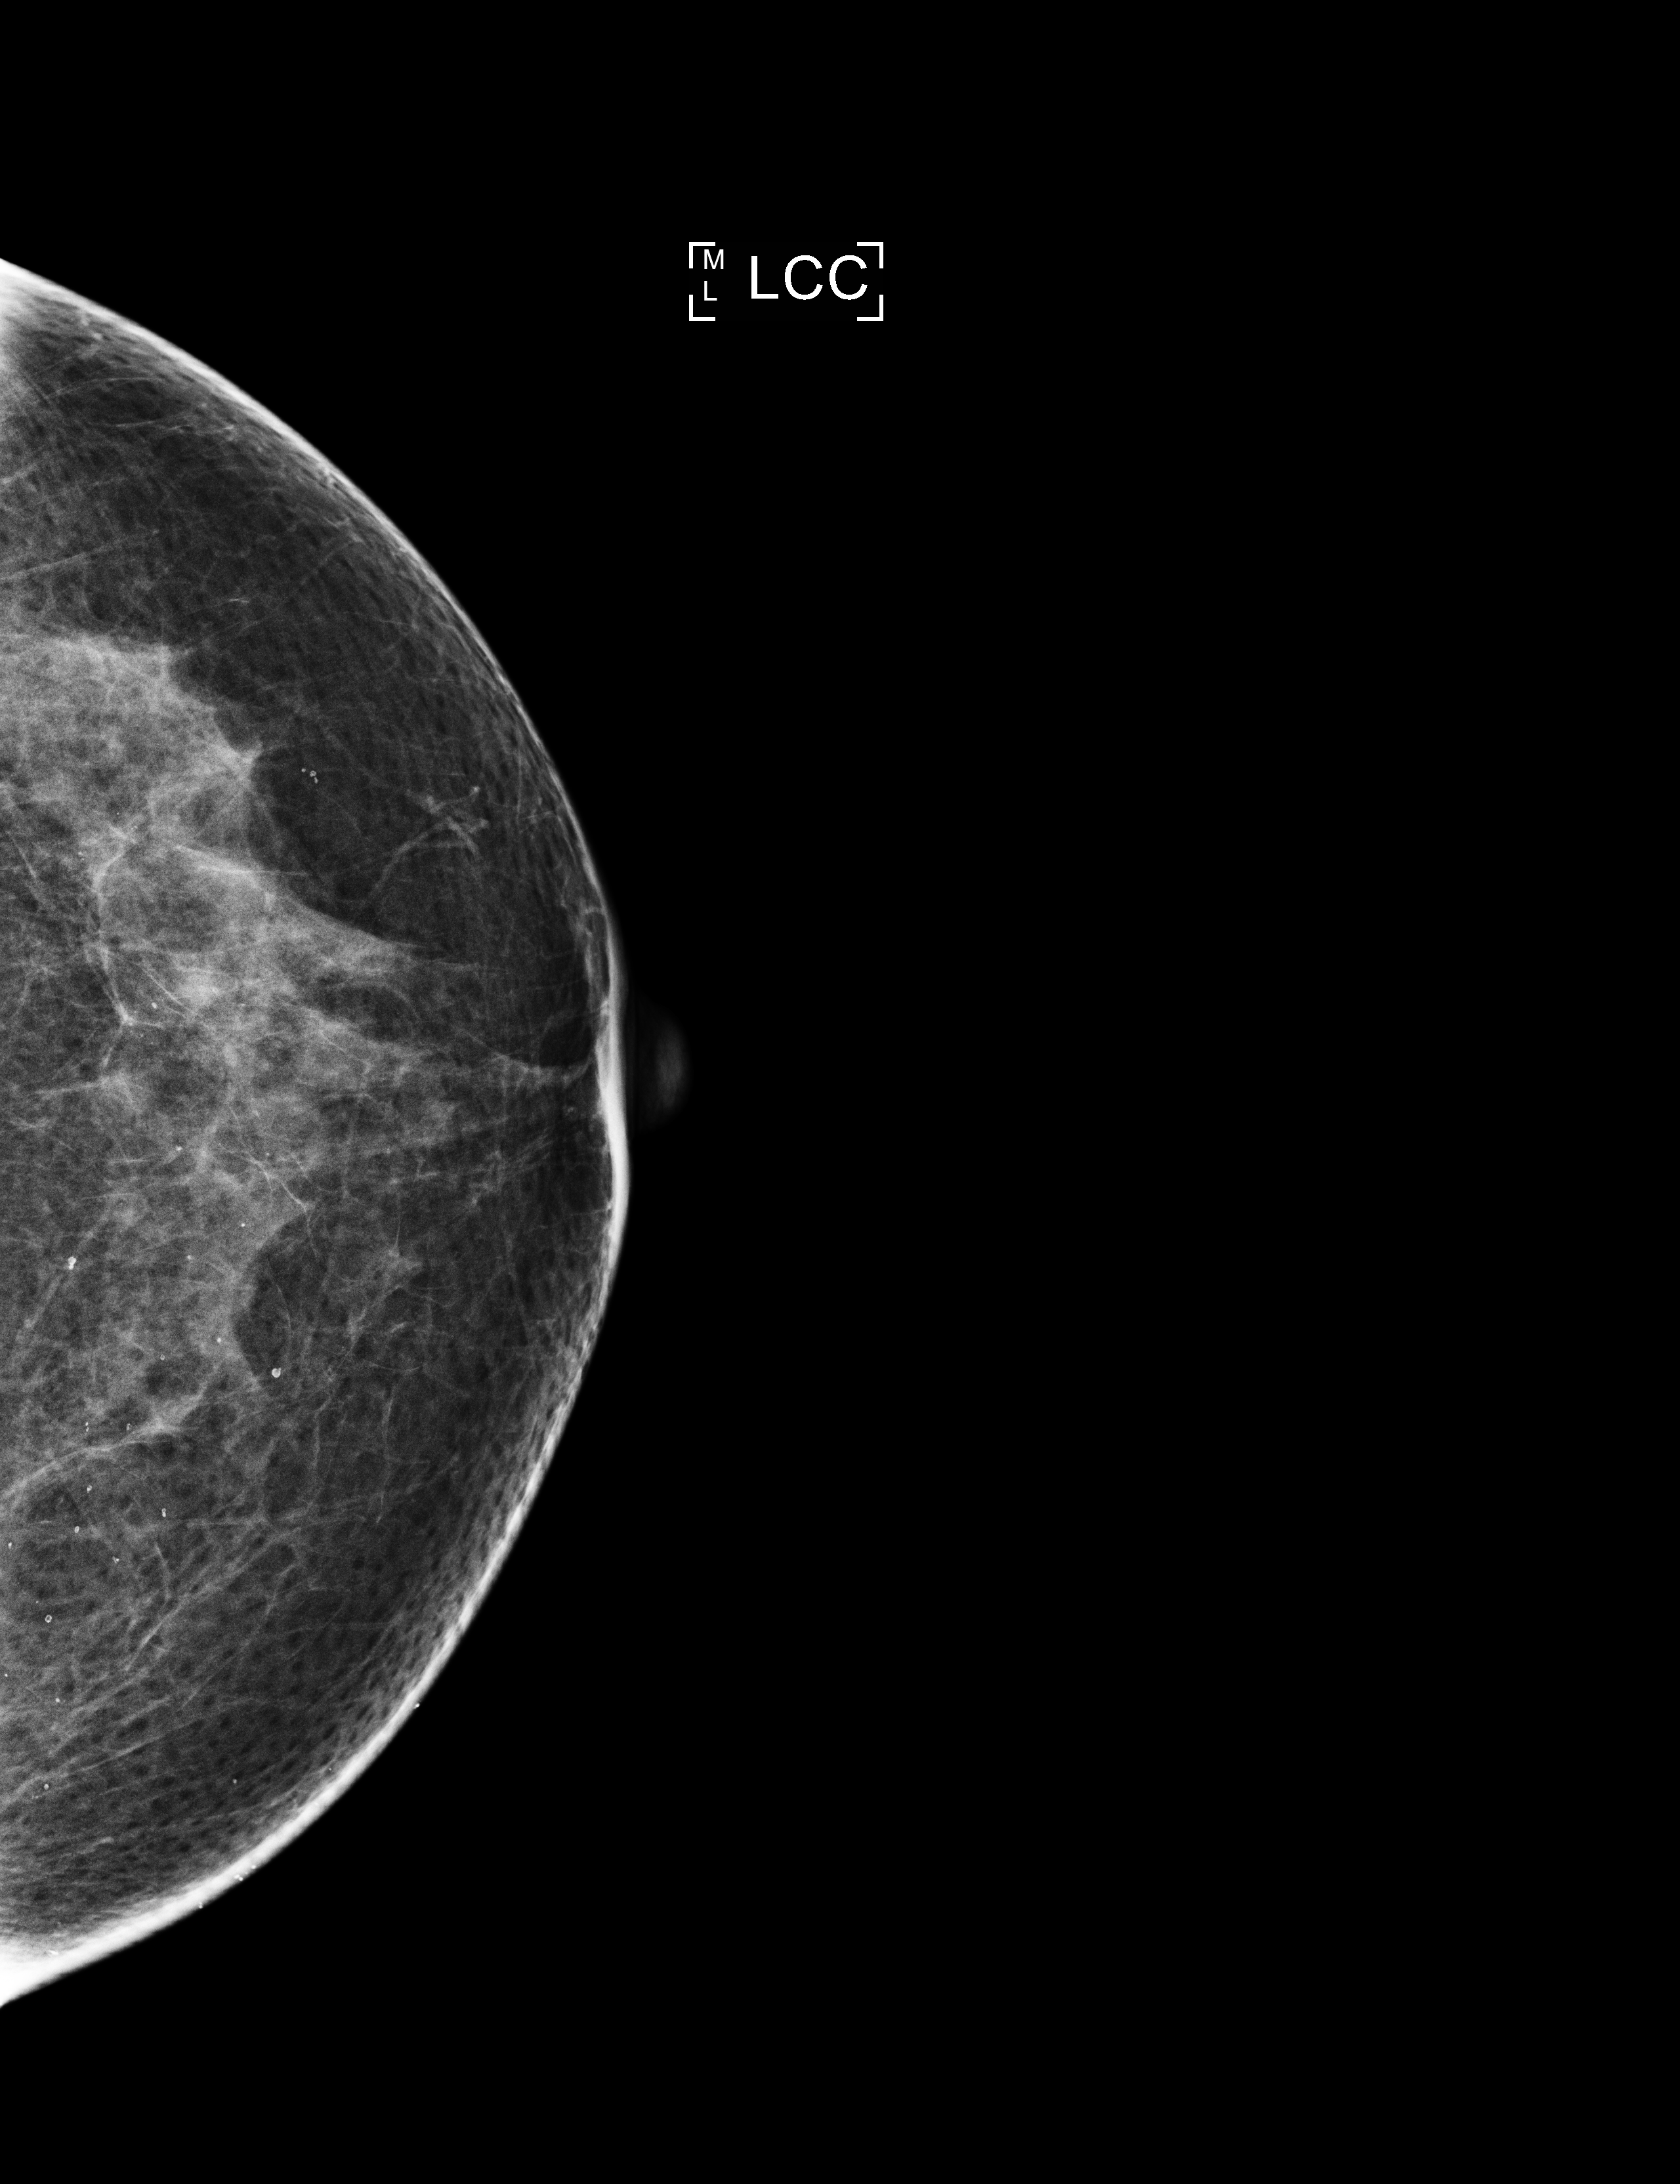
Digital mammogram (FFDM), left breast, craniocaudal (CC) view, screening examination, system: Selenia Dimensions. Patient aged 68 years (female).
Final BI-RADS assessment for this screening round (tomosynthesis exam, both breasts): category 2.